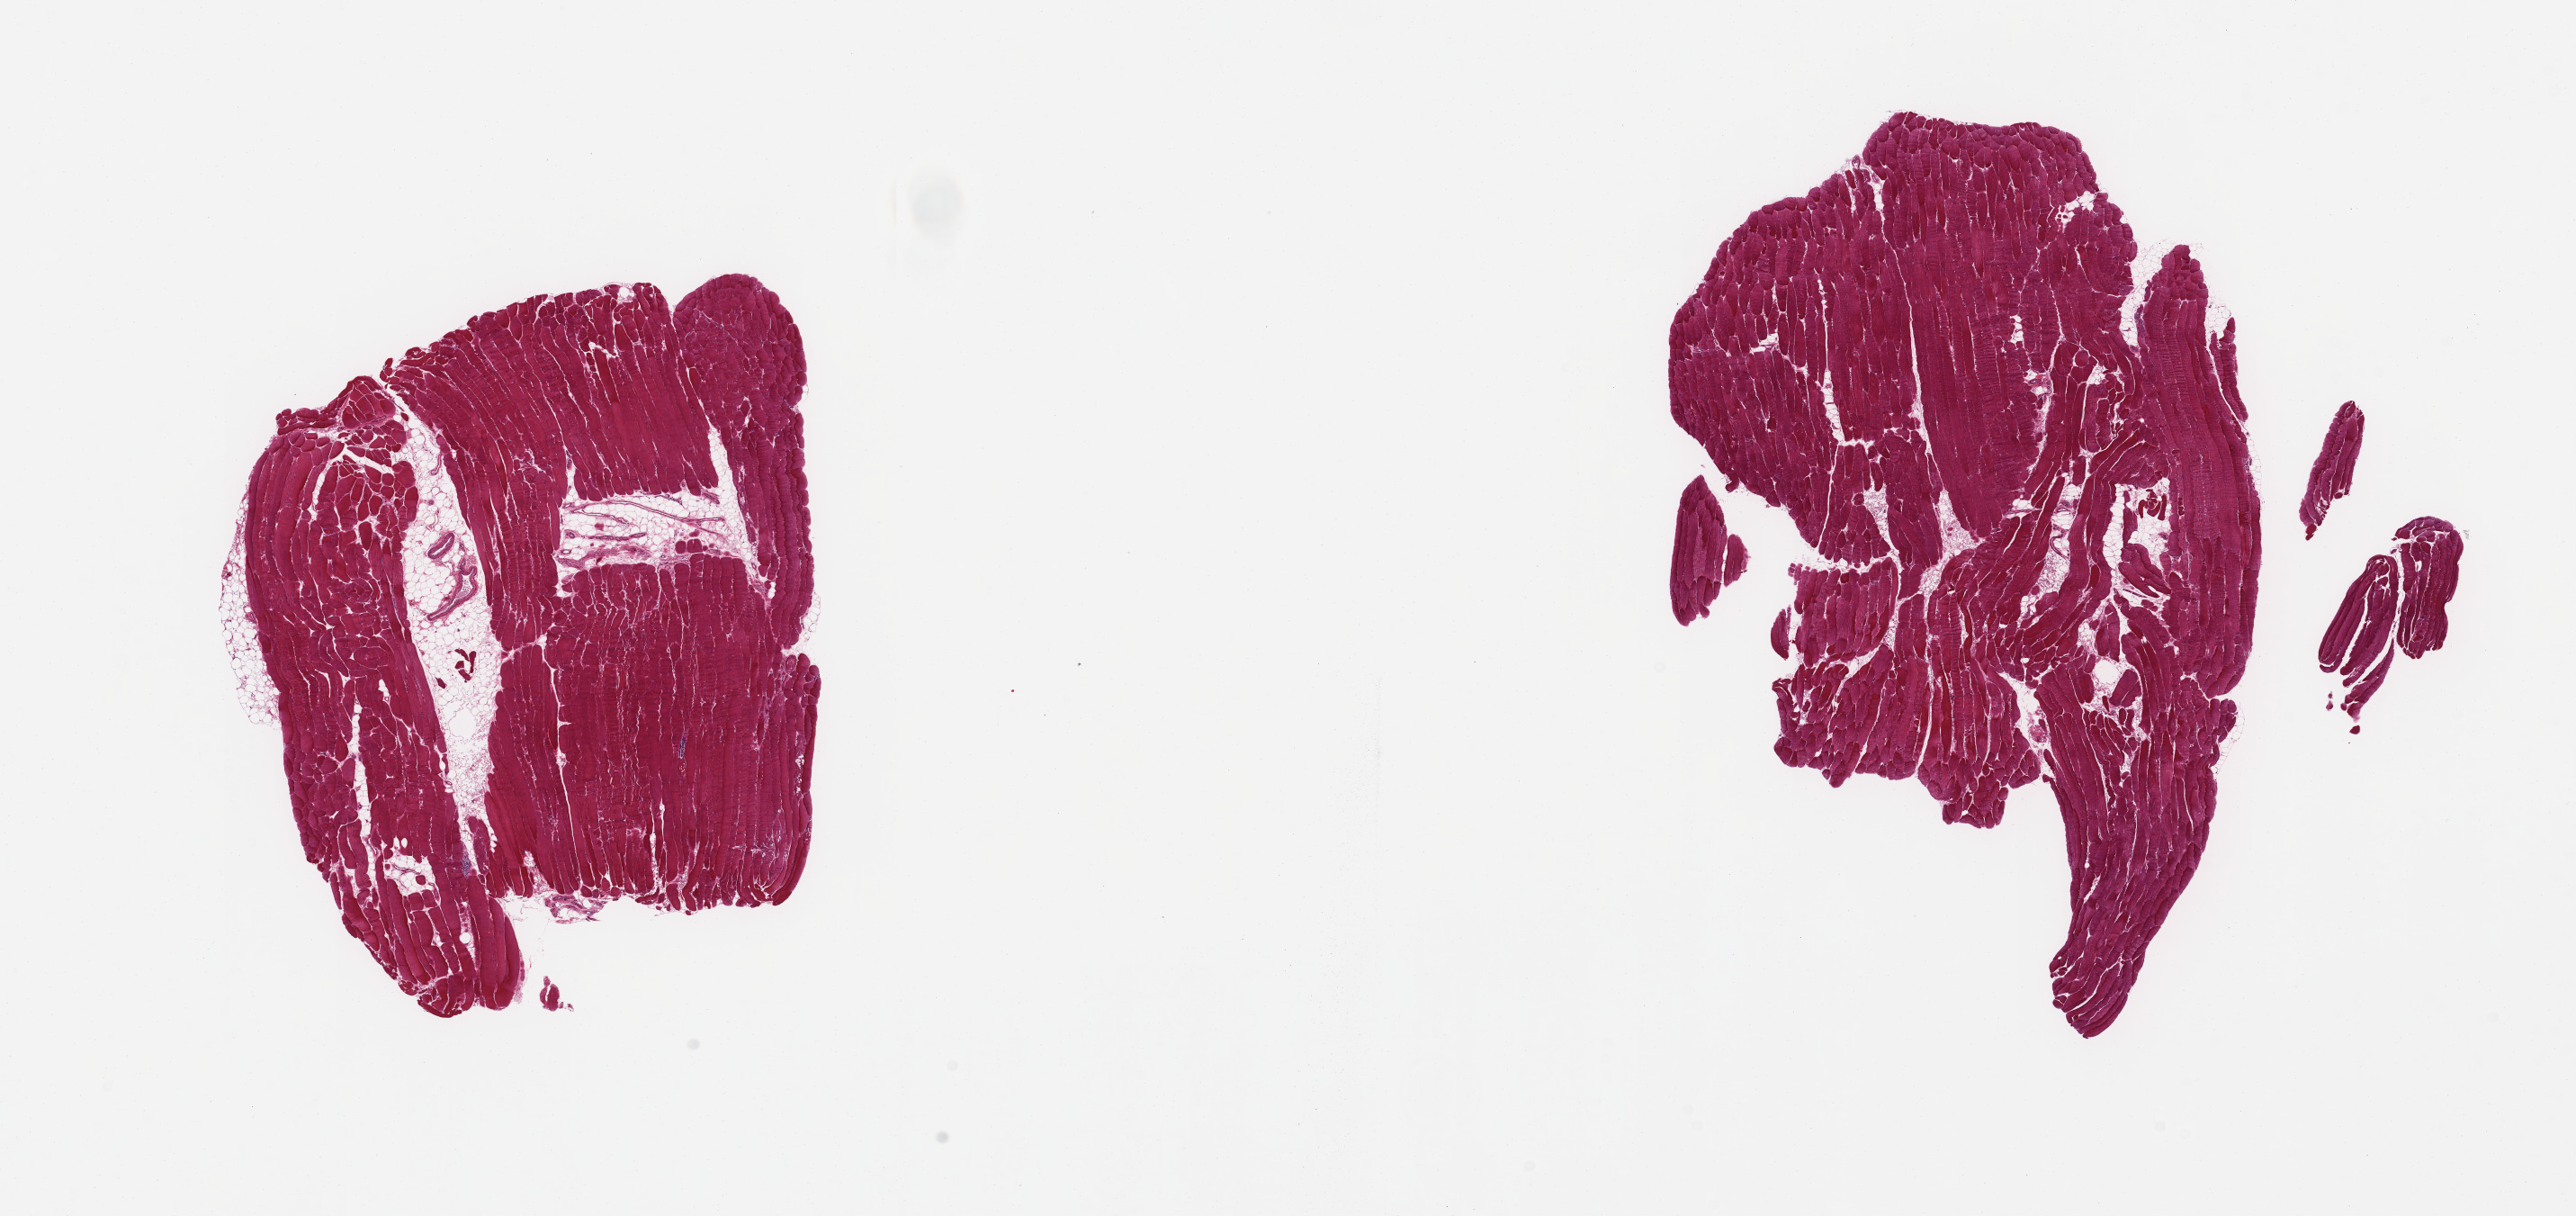
Whole-slide image, hematoxylin and eosin (H&E) stain, brightfield, whole scanned area (about 22.6 x 10.7 mm) shown as a low-resolution overview. PAXgene-fixed paraffin-embedded (PFPE) section. Target tissue: skeletal muscle. Tissue donor sample. Donor: female.
* pathologist's review note for this sample: 2 pieces; include from 5-15% inteernal (mostly) and external fat